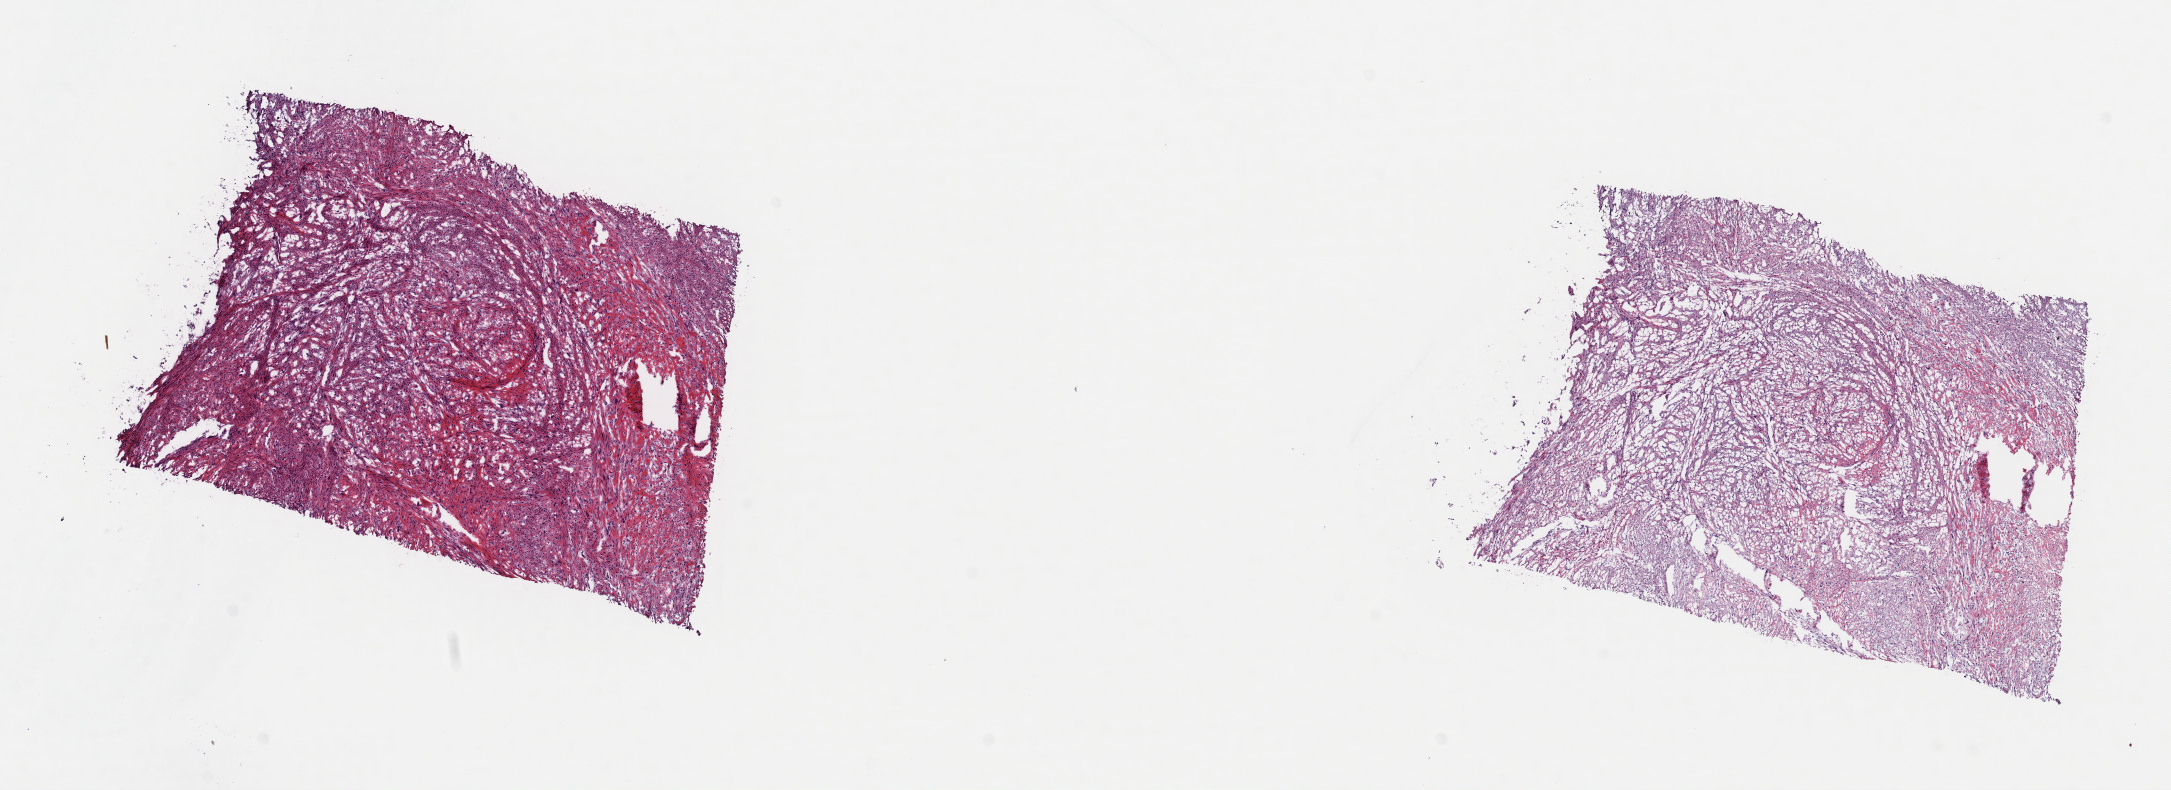
Digitized H&E-stained tissue section (whole slide) — shown as a low-resolution overview of the whole scanned area (about 17.2 x 6.2 mm, slide scanned at 40x), frozen section from the top of the tissue portion, retroperitoneum and peritoneum, primary tumour sample. Male patient; age at initial diagnosis 34 years.
Pathologic diagnosis: Dedifferentiated liposarcoma (retroperitoneum).